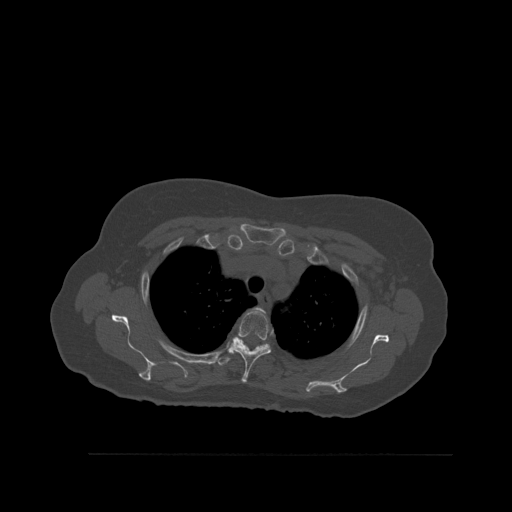
CT including the spine, one axial slice. Slice 418 of 527 in the series (ordered by position). Bone window (W 1800 / L 400 HU). 512 × 512 image matrix, field of view 470 × 470 mm. Patient: female, 73 years. Case-level facts recorded for this patient, not image findings: primary cancer: breast; vertebrae with lytic lesions (as recorded): L2.
Outlined on this slice (semi-automatic segmentation, software-assisted and operator-edited):
- T2 vertebra: bounding box (x1, y1, x2, y2) in pixels: (251, 307, 265, 313)
- T3 vertebra: (229, 310, 271, 383)
- T4 vertebra: (218, 356, 231, 366)